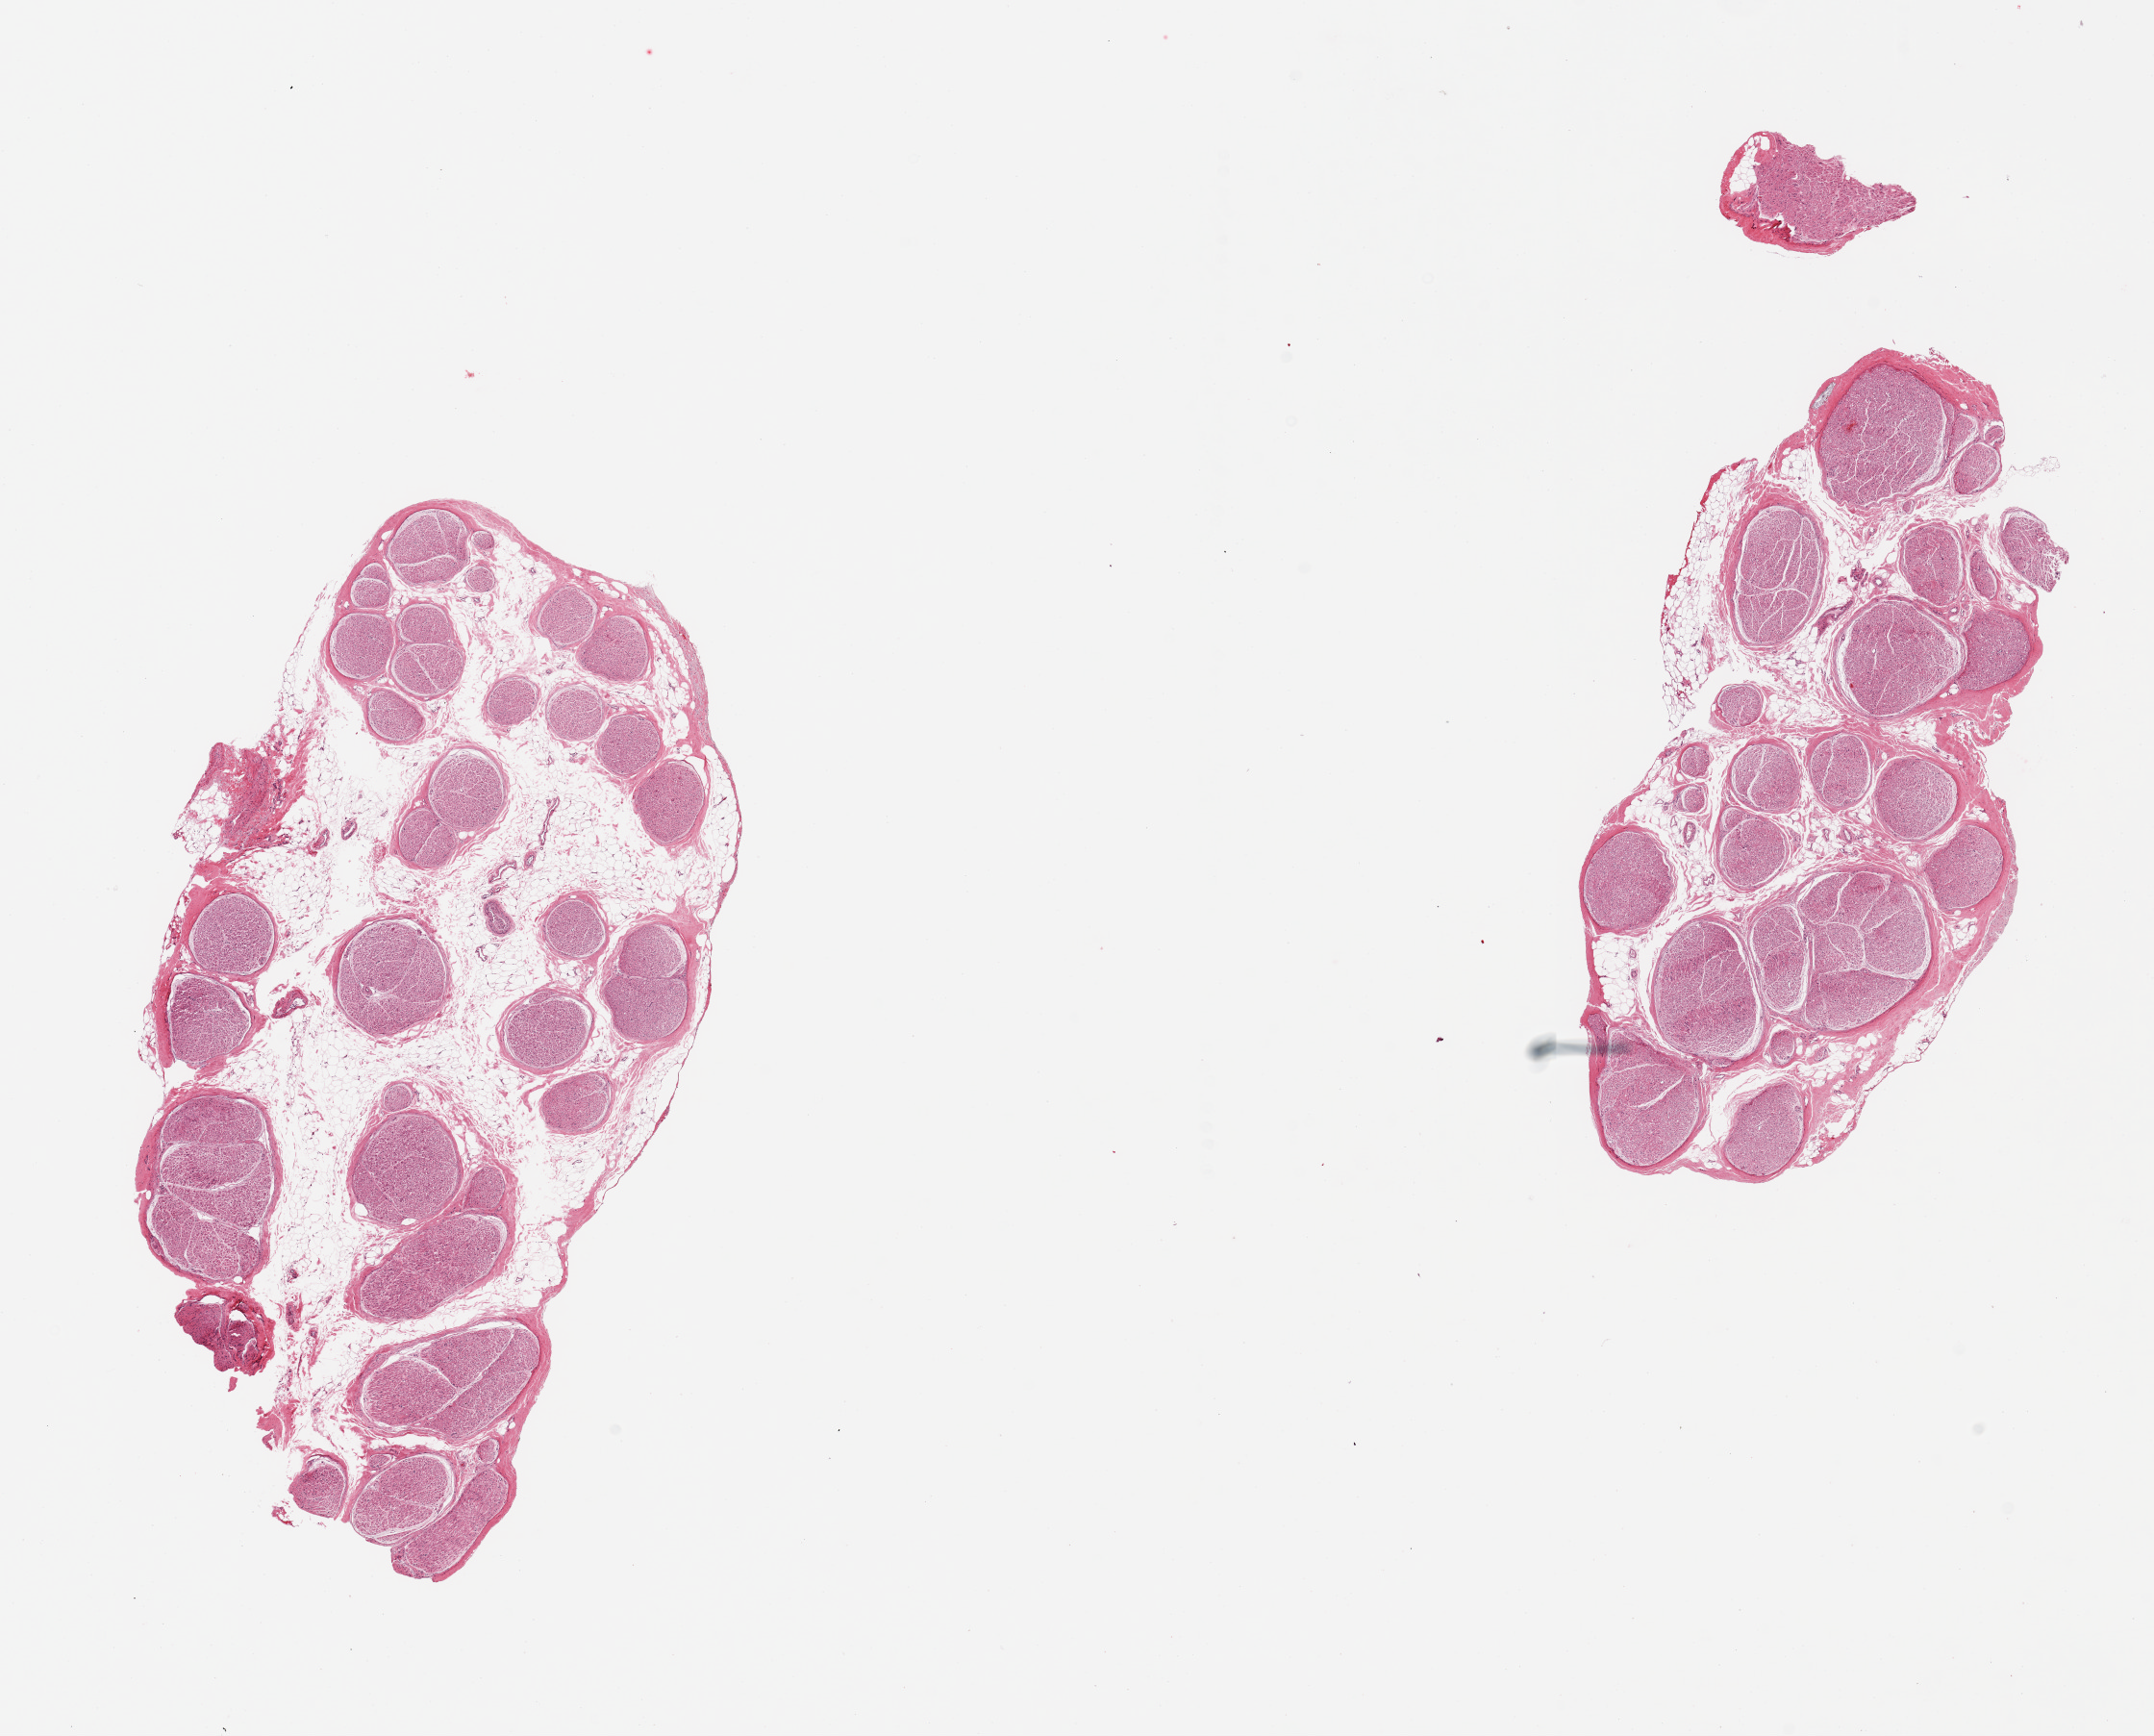
Whole-slide image, haematoxylin and eosin stain, low-resolution overview of the scanned area, about 17.7 x 14.3 mm (from a 20x scan). PAXgene-fixed paraffin-embedded (PFPE) section. Section of tibial nerve (target tissue). Tissue donor sample. Donor sex: female.
Pathologist's review note for this sample: 2 pieces, clean sections.